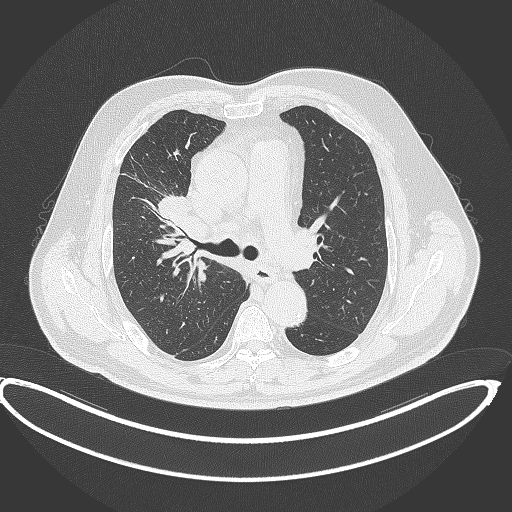
Chest CT, one axial slice; position 263 of 390 along the scan axis; reconstruction kernel B70f; 120 kVp; lung window (W 1500 / L -600 HU); 512 × 512 image matrix, field of view 448 × 448 mm. Patient: male, 62 years. Case-level facts recorded for this patient, not image findings: clinical TNM (as recorded): T1c N3 M1c.
Annotated regions visible in this slice (bounding box drawn by a radiologist):
- lung tumour (recorded histology: adenocarcinoma): bounding box [x1, y1, x2, y2] px = [154, 193, 201, 235]